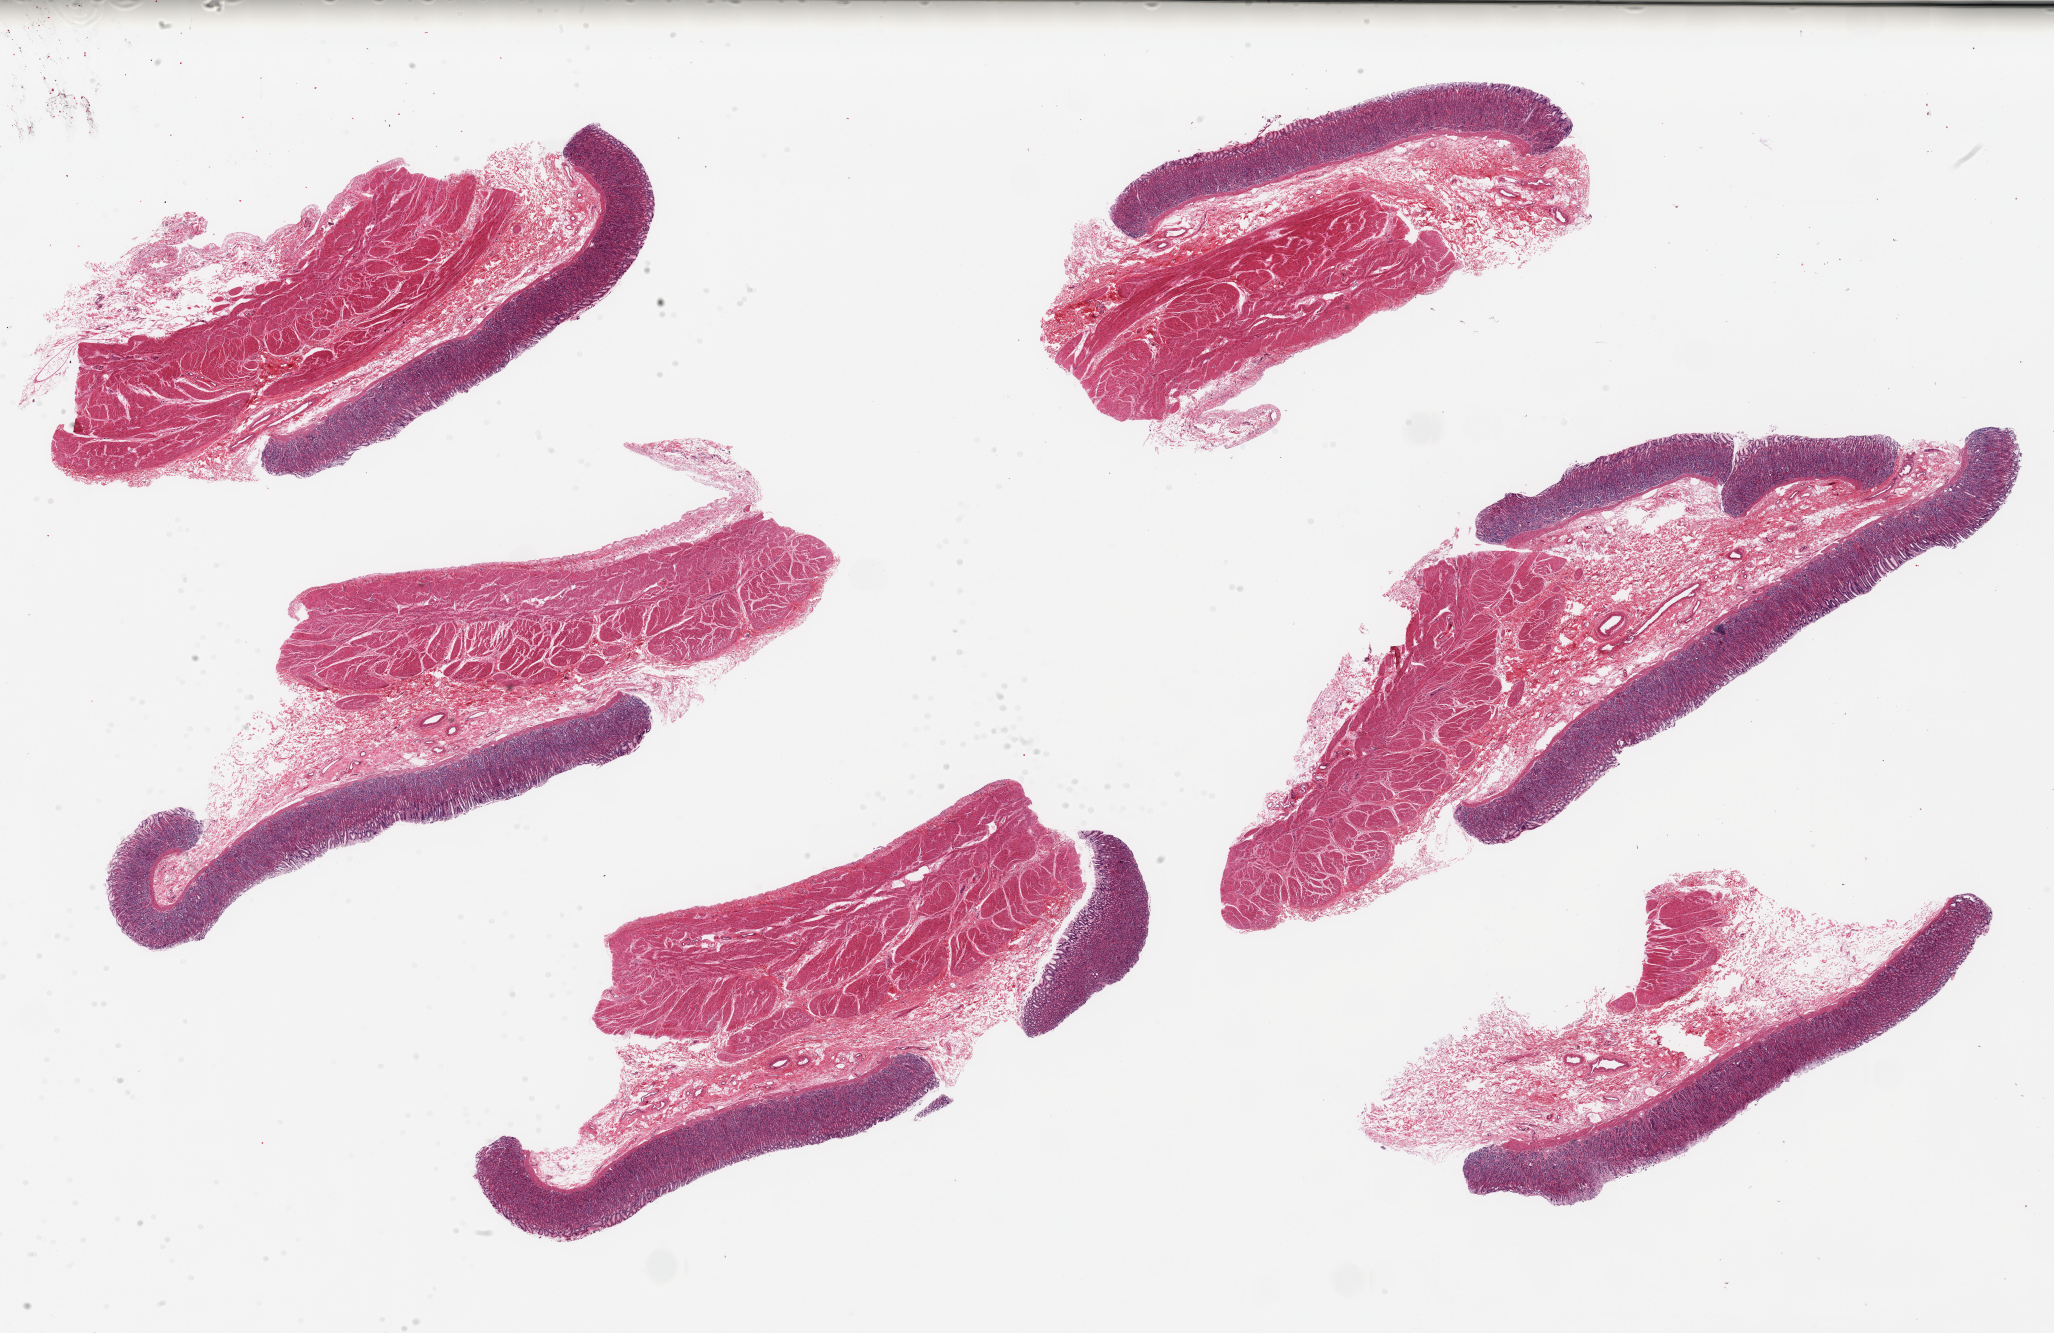
Haematoxylin and eosin whole-slide image, whole scanned area (about 32.5 x 21.1 mm, slide scanned at 20x) shown as a low-resolution overview; PAXgene-fixed, paraffin-embedded tissue; section of stomach (target tissue); tissue donor sample. Female donor.
Review note (as recorded): 6 pieces, up to 10x4mm. mucosa varies in preservation from very good to moderate.